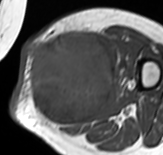
MRI of an extremity soft-tissue mass, one axial slice. MR volume resampled by the dataset authors to the PET/CT grid (not the native acquisition matrix). 3.27 mm slice thickness. 163 × 155 image matrix, field of view 159 × 151 mm. Female patient. Case-level facts recorded for this patient, not image findings: histological type: pleomorphic leiomyosarcoma; grade: high; site of the primary tumour: left thigh.
Outlined on this slice (expert contour drawn on MRI and transferred to this co-registered scan by the dataset authors):
- gross tumour volume including surrounding oedema: bounding box [x1, y1, x2, y2] px = [26, 31, 120, 130]
- gross tumour volume (mass): [26, 31, 116, 128]